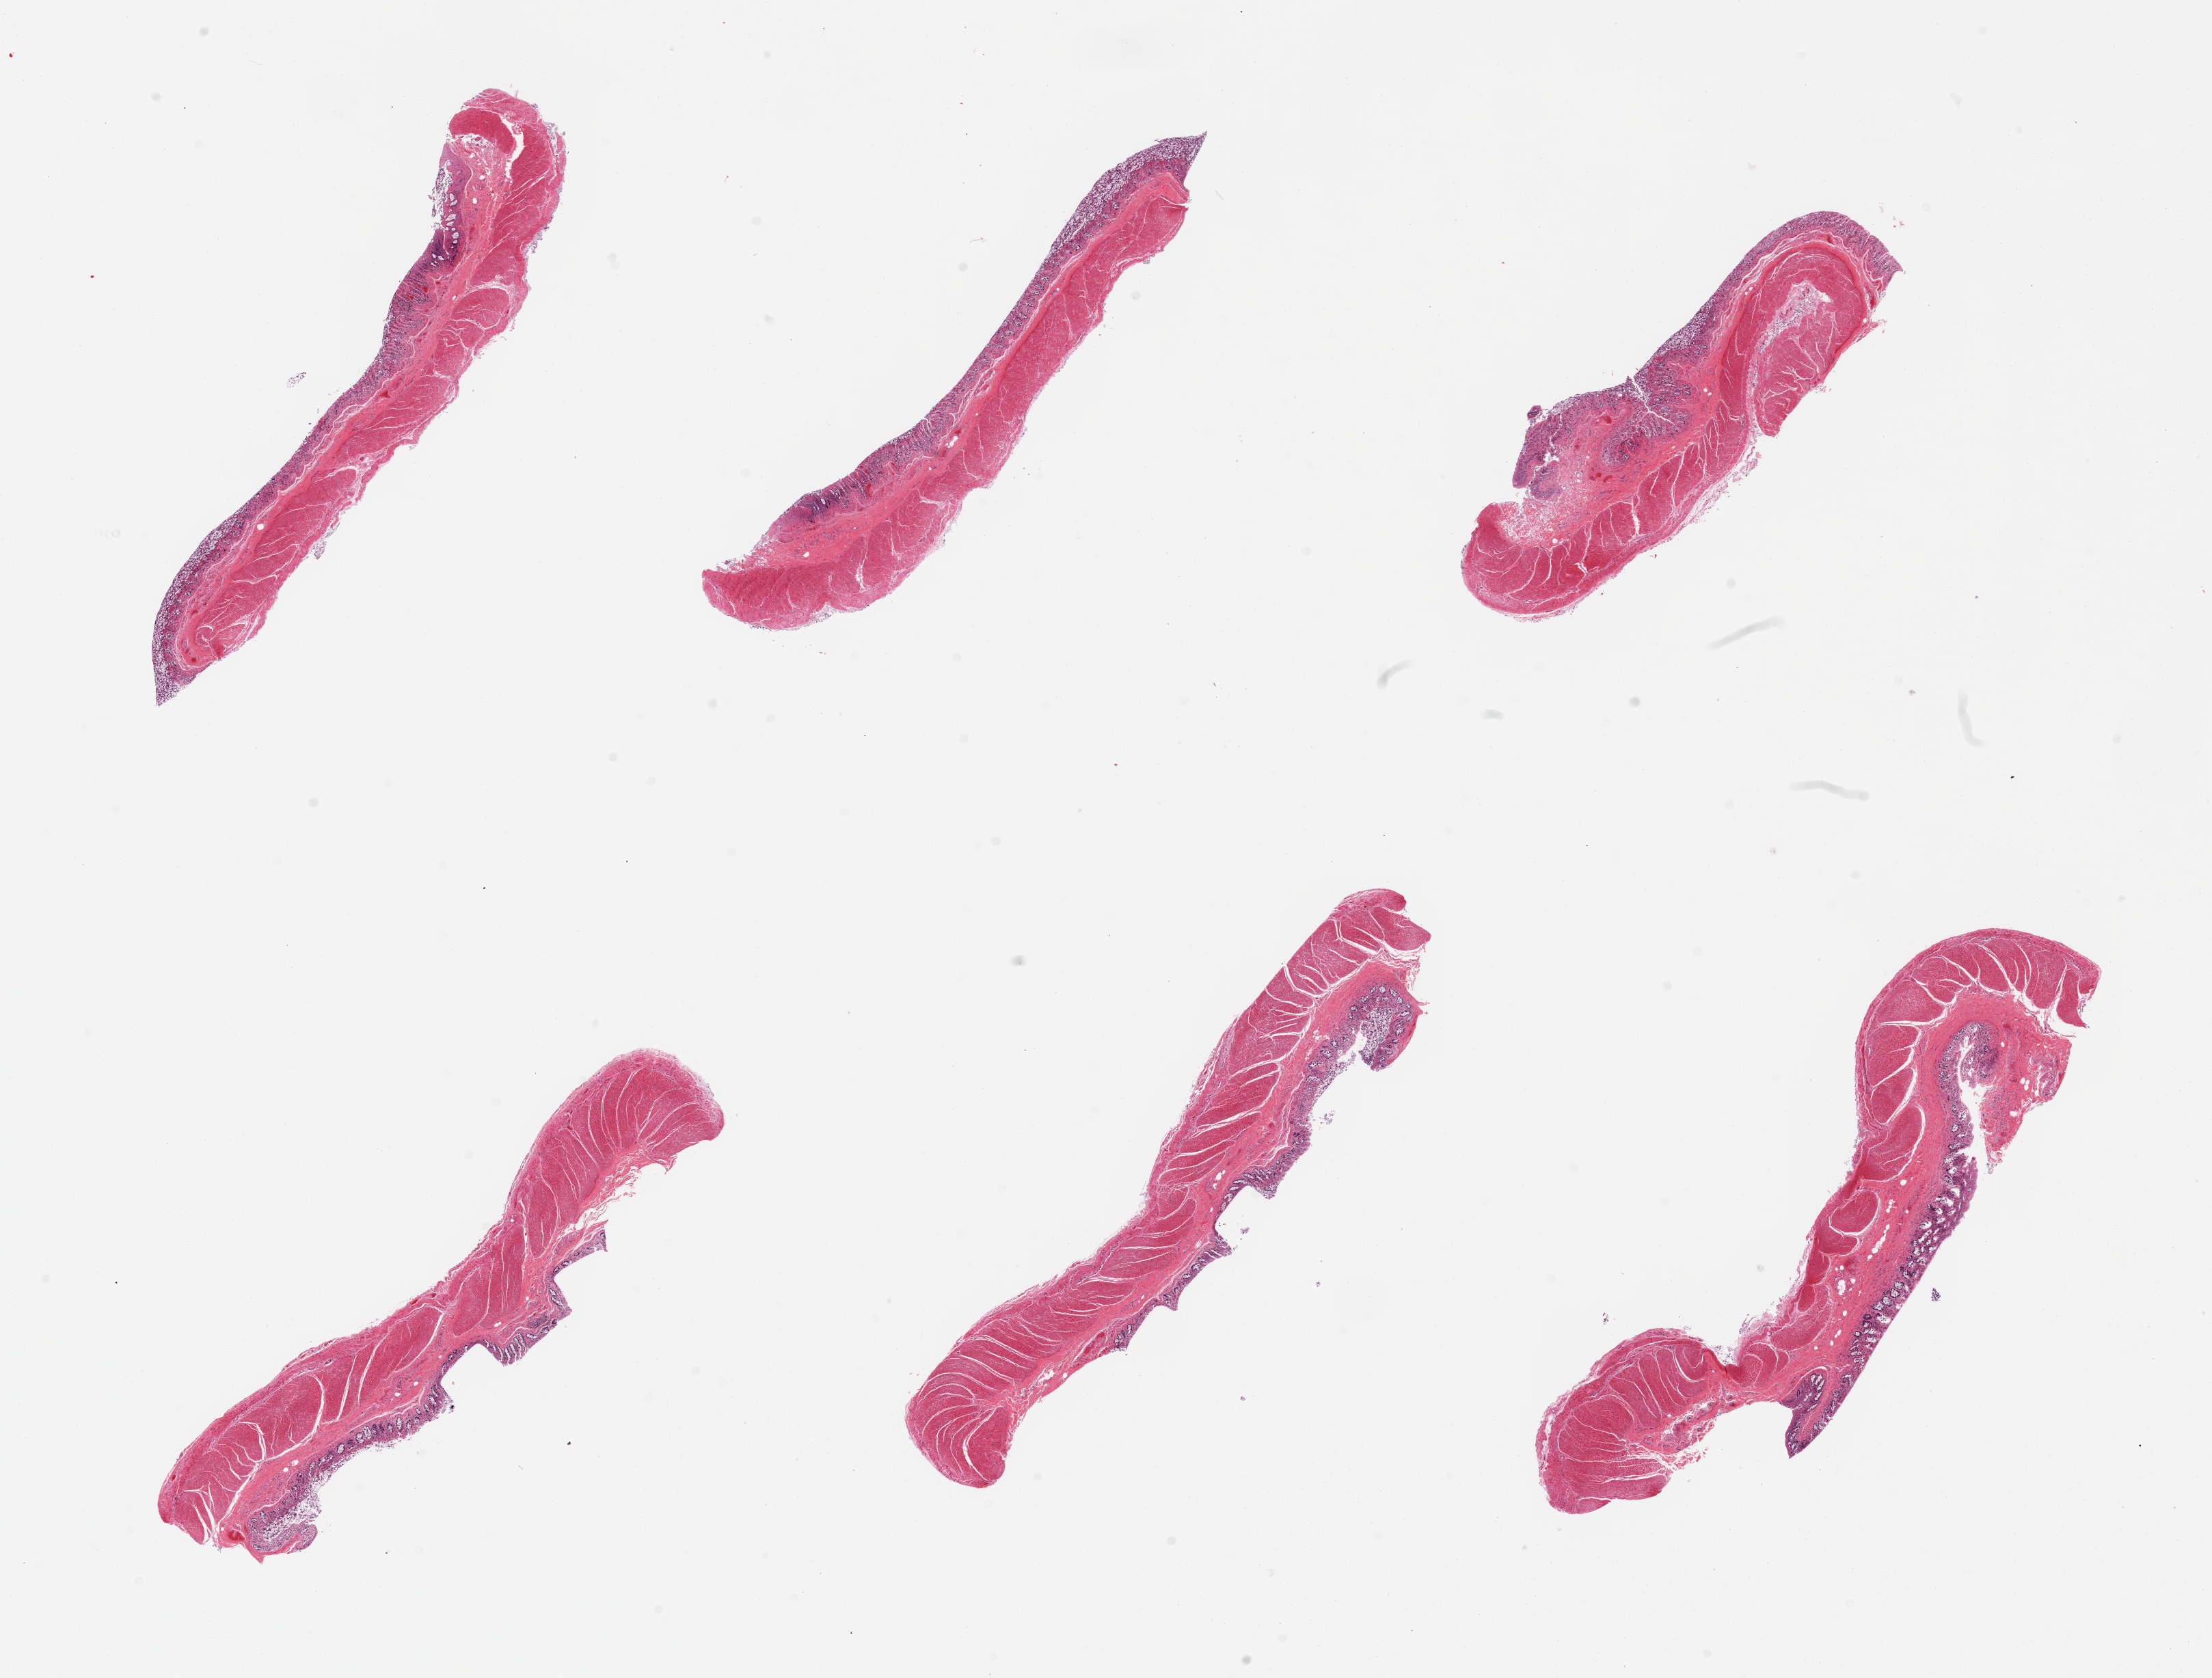
H&E whole-slide image, brightfield, shown as a low-resolution overview of the whole scanned area (about 25.6 x 19.4 mm). PAXgene-fixed paraffin-embedded (PFPE) section. Sampled site (target tissue): transverse colon. Tissue donor sample. Donor: female.
- reviewer comment on this tissue sample: 6 pieces, mucosa is ~30 % thickness but epithelial component is totaly autolyzed